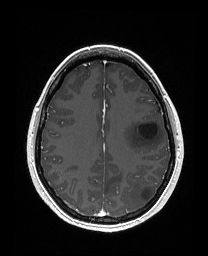
Brain MRI from a brain-tumour surgery series, one axial slice; slice 108 of 176 in the series (ordered by position); T1-weighted post-contrast; 1 mm slice thickness; 208 × 256 image matrix, field of view 203 × 250 mm. Case-level facts recorded for this patient, not image findings: histopathology: Astrocytoma; WHO grade: 3; IDH mutation: yes; tumour location: Left Frontal.
Outlined on this slice (outlined manually by an expert reader):
- tumour: bounding box [x1, y1, x2, y2] px = [123, 120, 164, 153]